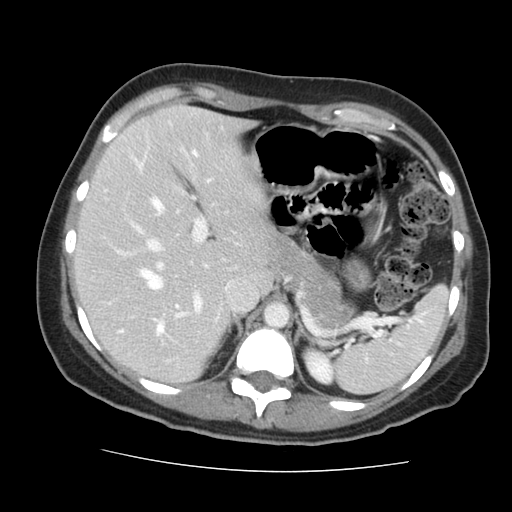
Contrast-enhanced abdominal CT, one axial slice; position 102 of 144 along the scan axis; 120 kVp; intravenous contrast given; soft-tissue window (W 400 / L 40 HU); 512 × 512 image matrix, field of view 333 × 333 mm. Female patient, age 46 years. From the clinical record (not read from this slice): diagnosis: colorectal cancer liver metastases, imaged before liver resection; multiple liver metastases: no; largest metastasis: 2.8 cm; disease in both lobes: no.
Structures marked on this image (expert manual segmentation):
- hepatic veins: bounding box (x1, y1, x2, y2) in pixels: (133, 159, 178, 307)
- liver: (78, 106, 272, 382)
- planned liver remnant (the part of the liver to remain after resection): (78, 106, 272, 382)
- portal vein (with intrahepatic branches): (116, 192, 208, 334)